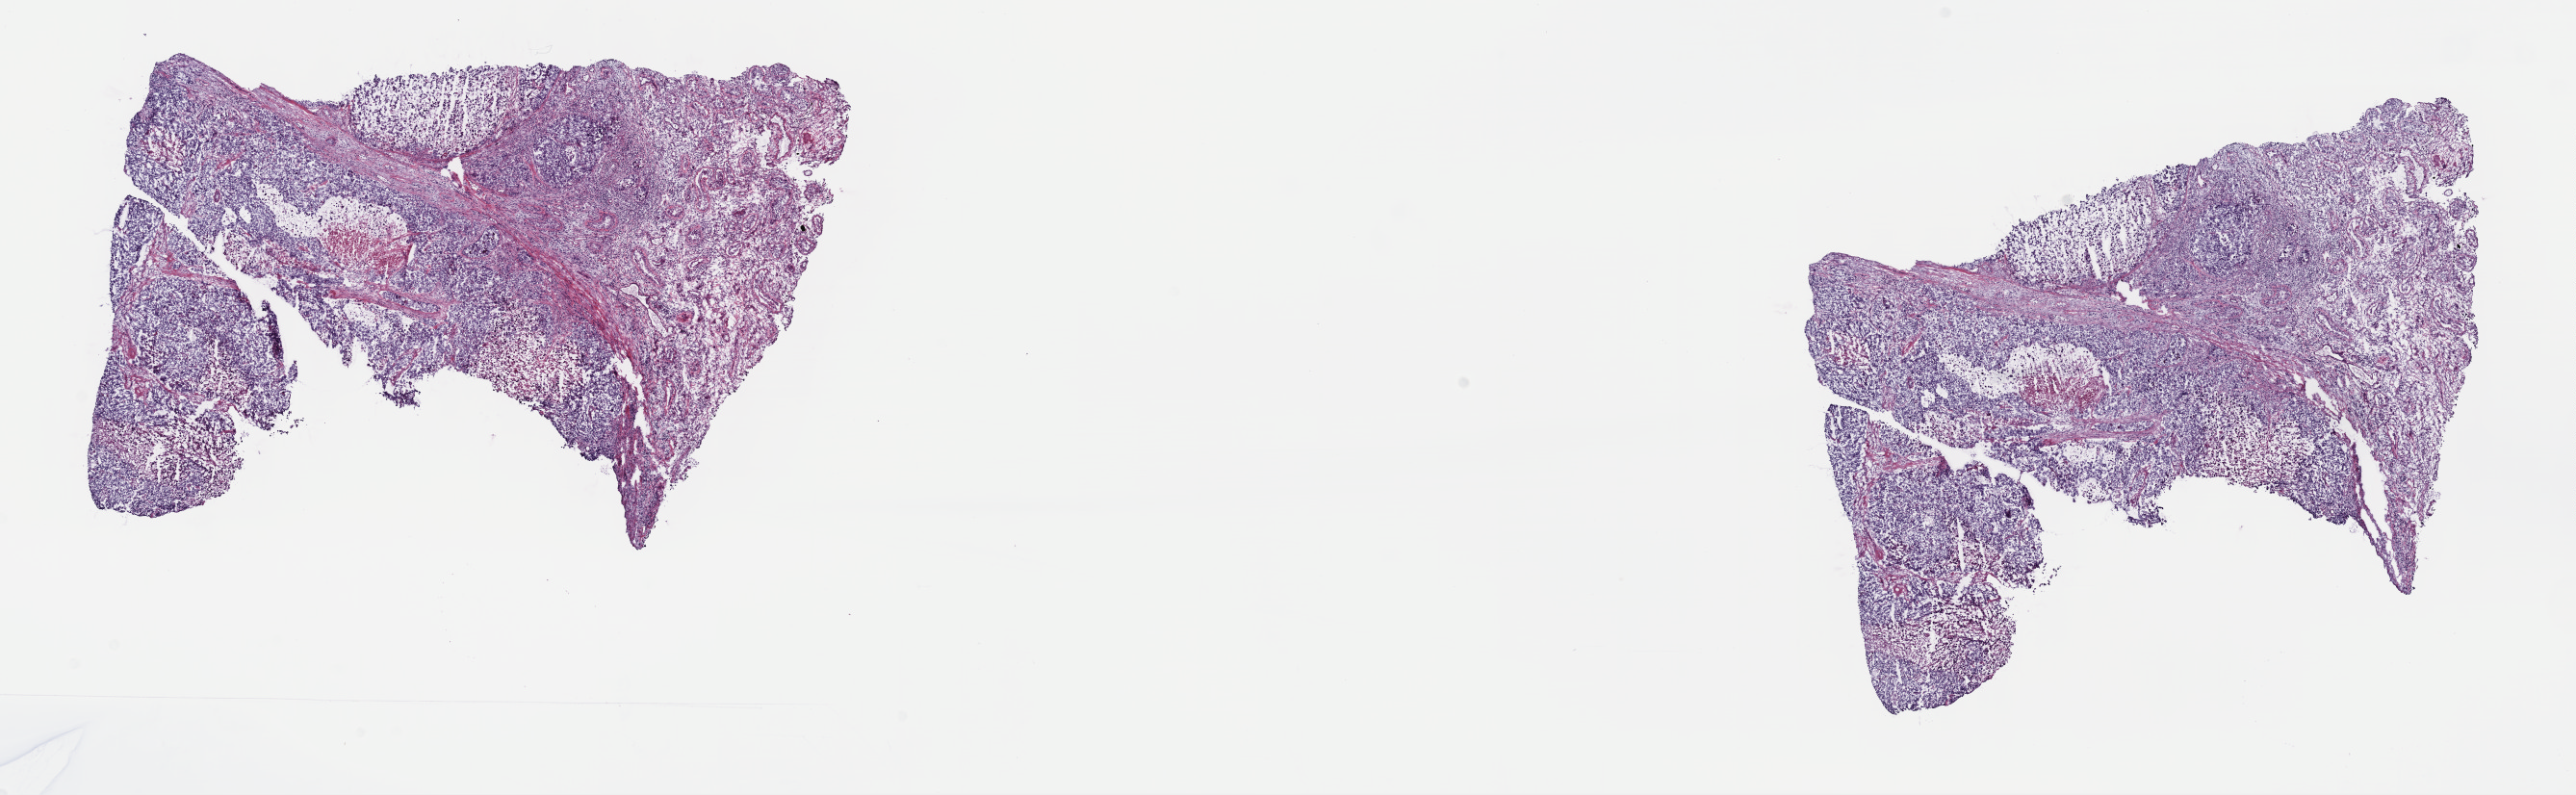
Digitized Hematoxylin and eosin (H&E) stained tissue section (whole slide) — whole scanned area (about 21.6 x 6.7 mm, from a 40x scan) shown as a low-resolution overview; frozen section from the top of the tissue portion; sample: primary tumour, testis. Male patient; age at initial diagnosis 33 years. Pathologist review of this section (percent, as recorded): tumour cells 95%, tumour nuclei 60%, normal cells 0%, stromal cells 0%, necrosis 5%. Inflammatory infiltration, as recorded: lymphocyte infiltration 4%, monocyte infiltration 0%, neutrophil infiltration 0%.
AJCC pathologic stage: IIA (7th edition). Pathologic diagnosis: Embryonal carcinoma, NOS. Laterality: left.